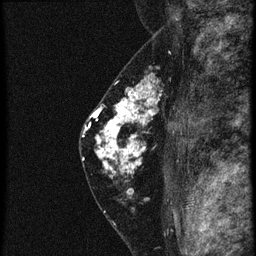
Breast MRI (dynamic contrast-enhanced), one sagittal slice. Slice 37 of 60 in the series (ordered by position). 4 images stored at this slice position (order not interpretable as contrast timing). 1.5 T. TE 4.2 ms, TR 20.4 ms. 256 × 256 image matrix, field of view 180 × 180 mm. Female patient, age 46 years. Case-level facts recorded for this patient, not image findings: setting: breast cancer imaged before/during neoadjuvant chemotherapy; receptor status: triple-negative.
Annotated regions visible in this slice (semi-automatic segmentation, software-assisted and operator-edited):
- analysis volume of interest (the breast-tissue region the enhancement analysis was run in; not a lesion): bounding box (x1, y1, x2, y2) in pixels: (88, 82, 179, 185)
- tumour enhancement mask (voxels above the 90 % enhancement threshold inside the analysis volume of interest): (96, 82, 157, 175)